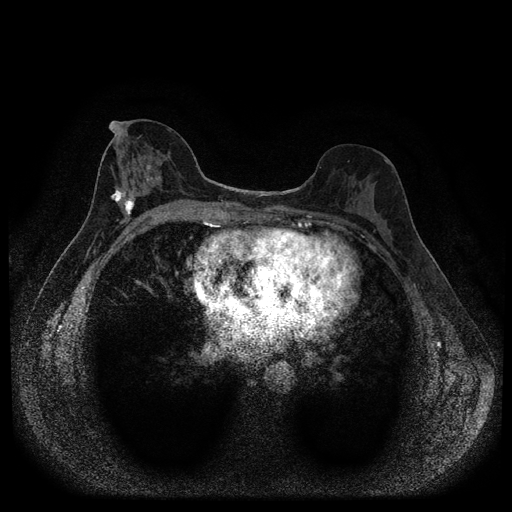
Breast MRI (dynamic contrast-enhanced, multi-phase), one axial slice; position 49 of 116 along the scan axis; dynamic contrast-enhanced series, time point 2 of 5 at this slice position (early post-contrast); 1.5 T; TE 2.7 ms, TR 5.4 ms; 2 mm slice thickness; 512 × 512 image matrix, field of view 330 × 330 mm. Female patient, age 49 years.
Structures marked on this image (semi-automatically segmented with operator editing):
- breast lesion (labelled 'tumour' in the annotation; benign lesions carry a separate 'benign' label): bounding box <110,187,136,222> (left, top, right, bottom; pixels)